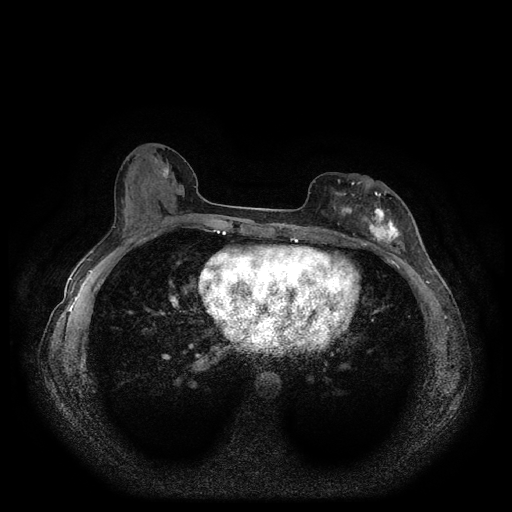
Breast MRI (dynamic contrast-enhanced, multi-phase), one axial slice. Slice 47 of 116 in the series (ordered by position). Dynamic contrast-enhanced series, time point 2 of 5 at this slice position (early post-contrast). 1.5 T. TE 2.6 ms, TR 5.3 ms. 512 × 512 image matrix, field of view 350 × 350 mm. Patient: female, 51 years.
Outlined on this slice (semi-automatically segmented with operator editing):
- breast lesion (labelled 'tumour' in the annotation; benign lesions carry a separate 'benign' label): bounding box [x1, y1, x2, y2] px = [331, 179, 405, 249]
- breast lesion (labelled benign in the annotation): [158, 160, 171, 182]